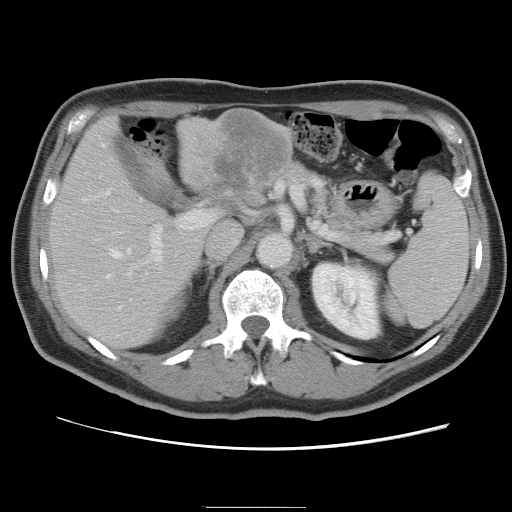
Contrast-enhanced abdominal CT, one axial slice. Slice 48 of 87 in the series (ordered by position). Intravenous contrast given. Soft-tissue window (W 400 / L 40 HU). 512 × 512 image matrix, field of view 363 × 363 mm. Male patient, age 63 years. Case-level facts recorded for this patient, not image findings: diagnosis: colorectal cancer liver metastases, imaged before liver resection; multiple liver metastases: no; largest metastasis: 9 cm.
Annotated regions visible in this slice (outlined manually by an expert reader):
- hepatic veins: bounding box <96,144,132,310> (left, top, right, bottom; pixels)
- liver: <50,109,293,351>
- planned liver remnant (the part of the liver to remain after resection): <50,146,203,351>
- portal vein (with intrahepatic branches): <113,208,215,277>
- liver metastasis: <214,113,283,200>